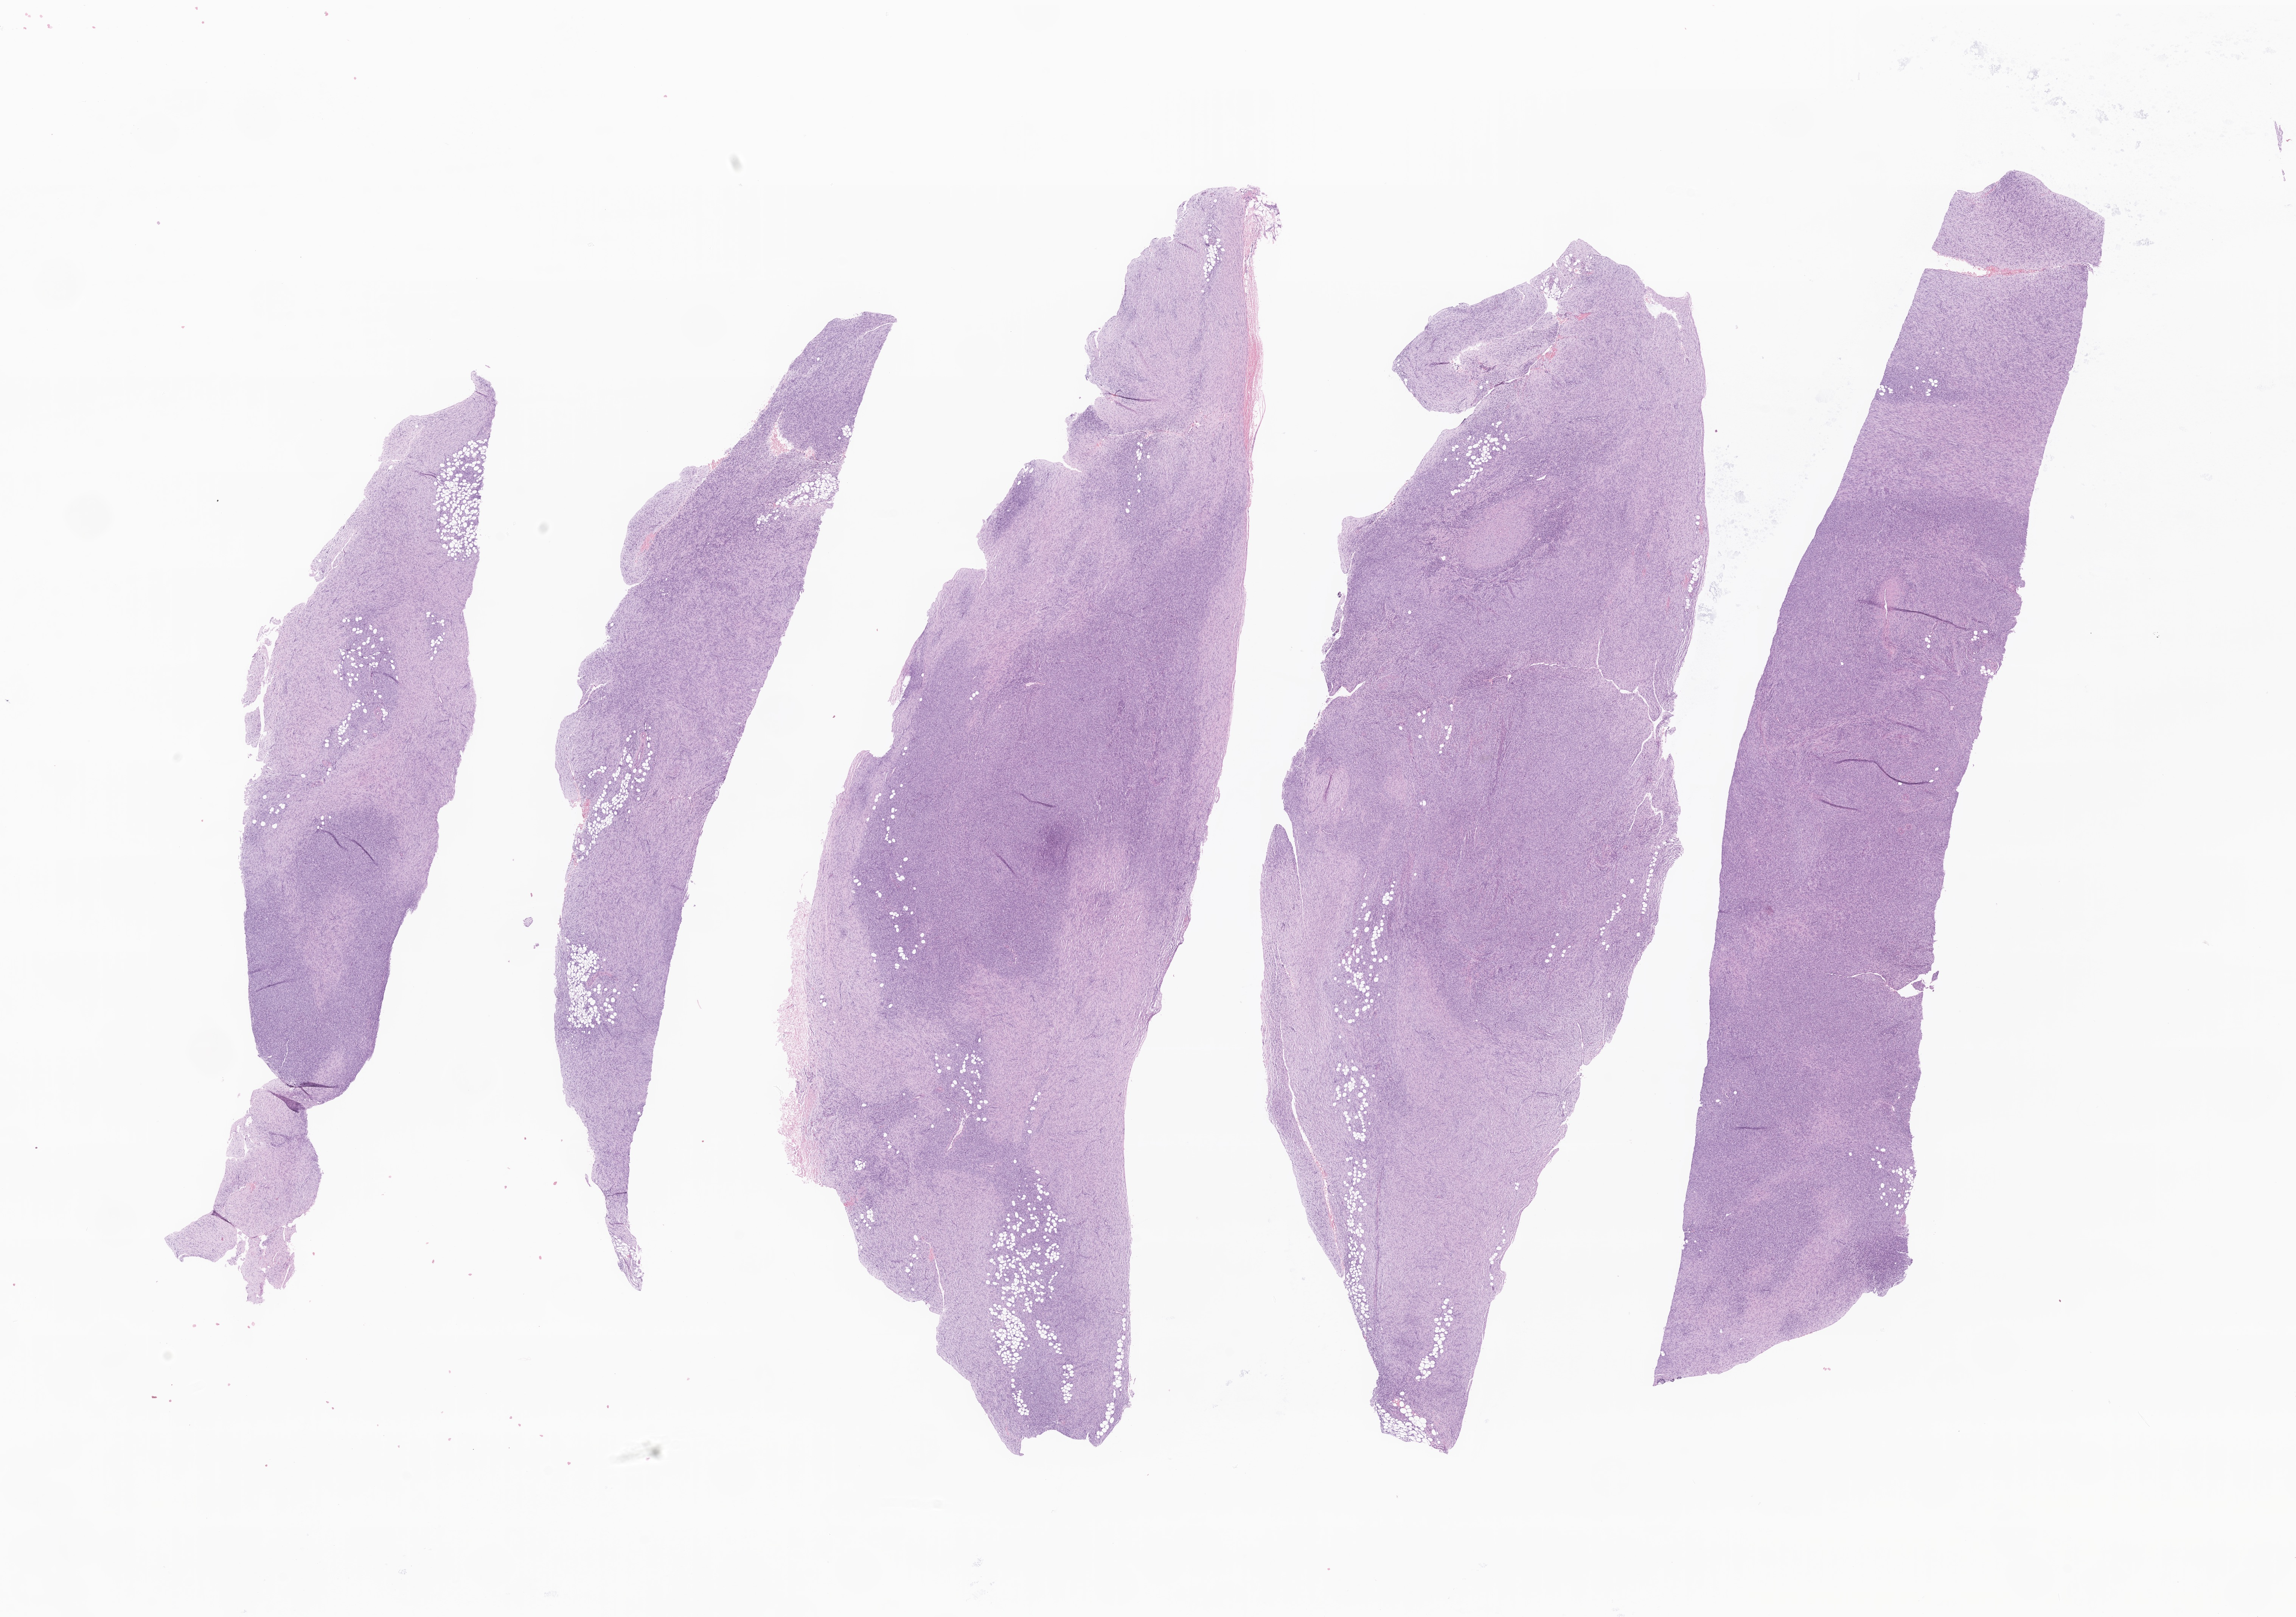
Hematoxylin and eosin (H&E) whole-slide image of tumor tissue from the lower limb — a low-resolution overview of the entire scanned area, about 25.6 x 18.0 mm, formalin-fixed paraffin-embedded section. Patient: female, age 104 months (8 years 8 months).
- recorded diagnosis: Dermatofibrosarcoma protuberans, fibrosarcomatous